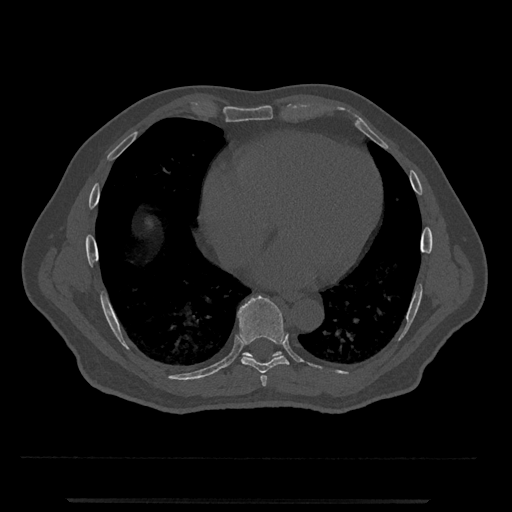
CT including the spine, one axial slice; position 617 of 797 along the scan axis; 120 kVp; bone window (W 1800 / L 400 HU); 0.5 mm slice thickness; 512 × 512 image matrix, field of view 419 × 419 mm. Patient: male, 63 years. From the clinical record (not read from this slice): primary cancer: prostate.
Annotated regions visible in this slice (semi-automatically segmented with operator editing):
- T7 vertebra: bounding box <260,375,267,387> (left, top, right, bottom; pixels)
- T8 vertebra: <237,295,289,374>
- T9 vertebra: <243,351,282,362>